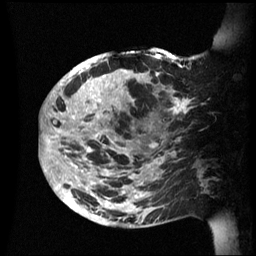
Breast MRI (dynamic contrast-enhanced), one sagittal slice. Slice 23 of 60 in the series (ordered by position). Dynamic contrast-enhanced series, image 2 of 3 at this slice position (ordered by acquisition). 1.5 T. TE 4.2 ms, TR 8.4 ms. 256 × 256 image matrix. Patient: female, 48 years.
Annotated regions visible in this slice (semi-automatic segmentation, software-assisted and operator-edited):
- analysis volume of interest (the breast-tissue region the enhancement analysis was run in; not a lesion): bounding box <42,47,202,228> (left, top, right, bottom; pixels)
- tumour enhancement mask (voxels above the 70 % enhancement threshold inside the analysis volume of interest): <42,54,185,227>